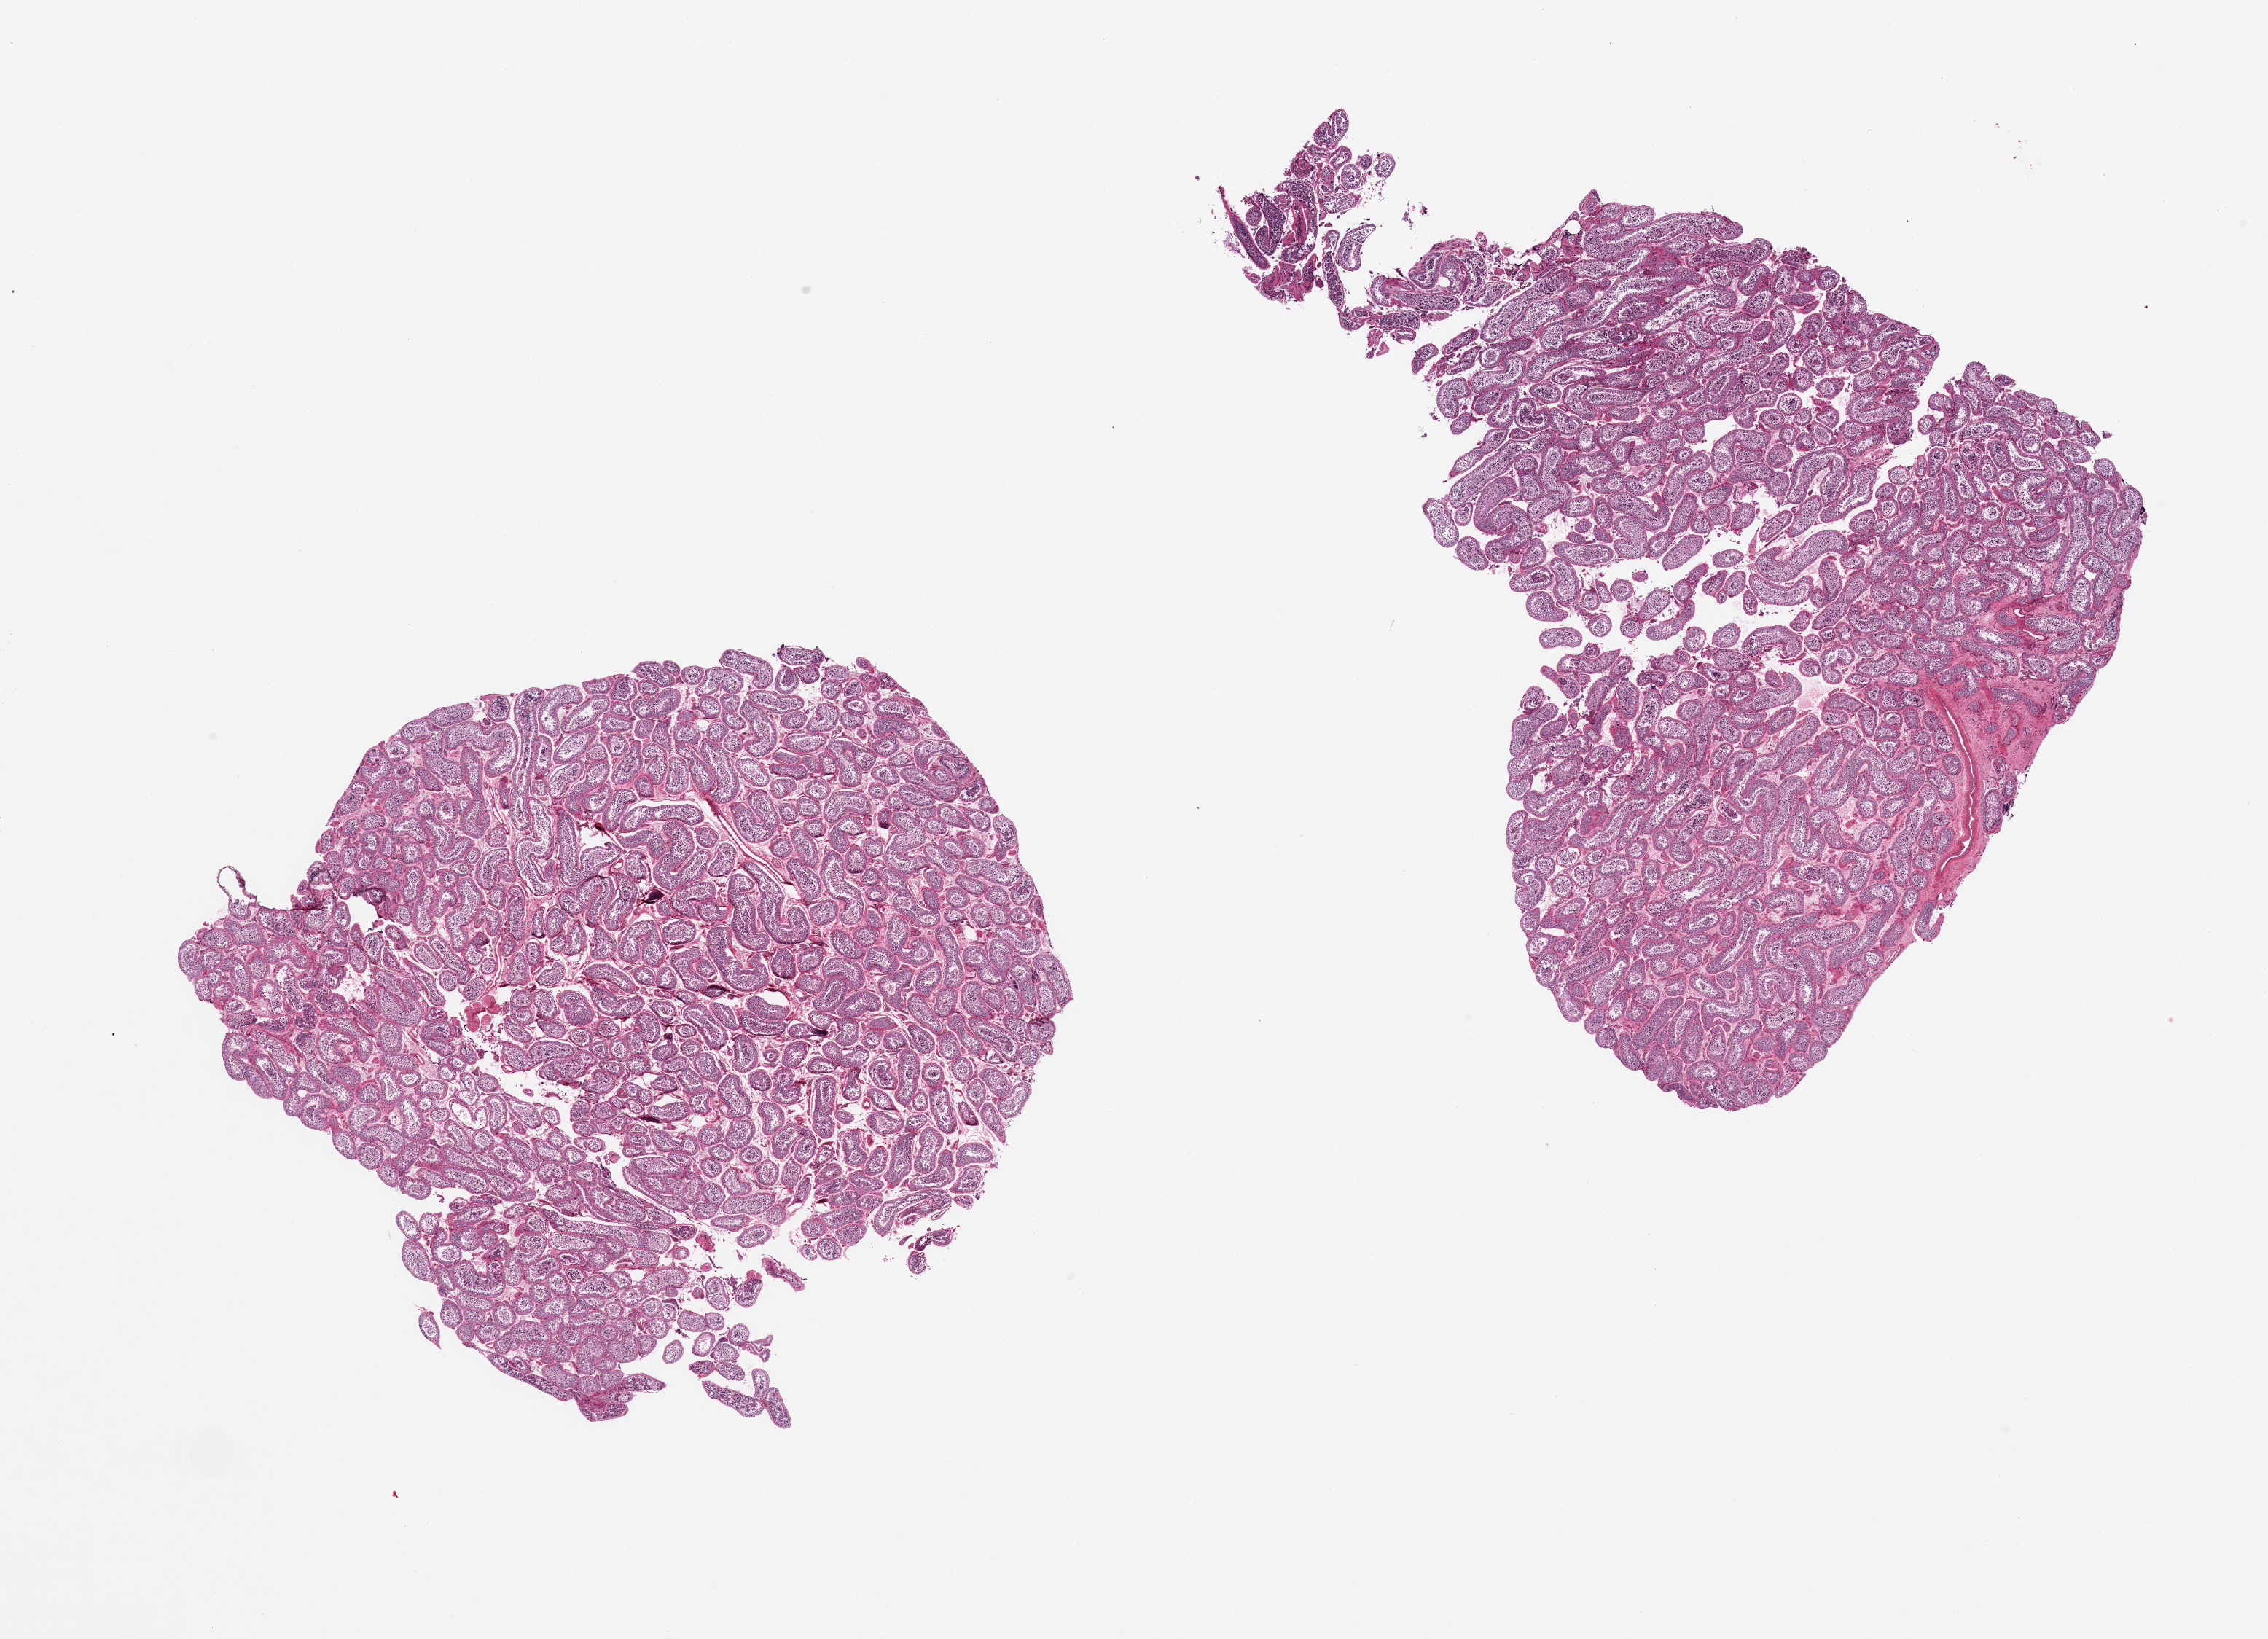
Digitized hematoxylin and eosin (H&E)-stained section, shown as a low-resolution overview of the whole scanned area (about 24.6 x 17.8 mm); PAXgene-fixed paraffin-embedded (PFPE) section; sampled site (target tissue): testis; donor tissue sample. Donor sex: male.
Reviewer comment on this tissue sample: 2 pieces, spermatogenesis present, normal levels.